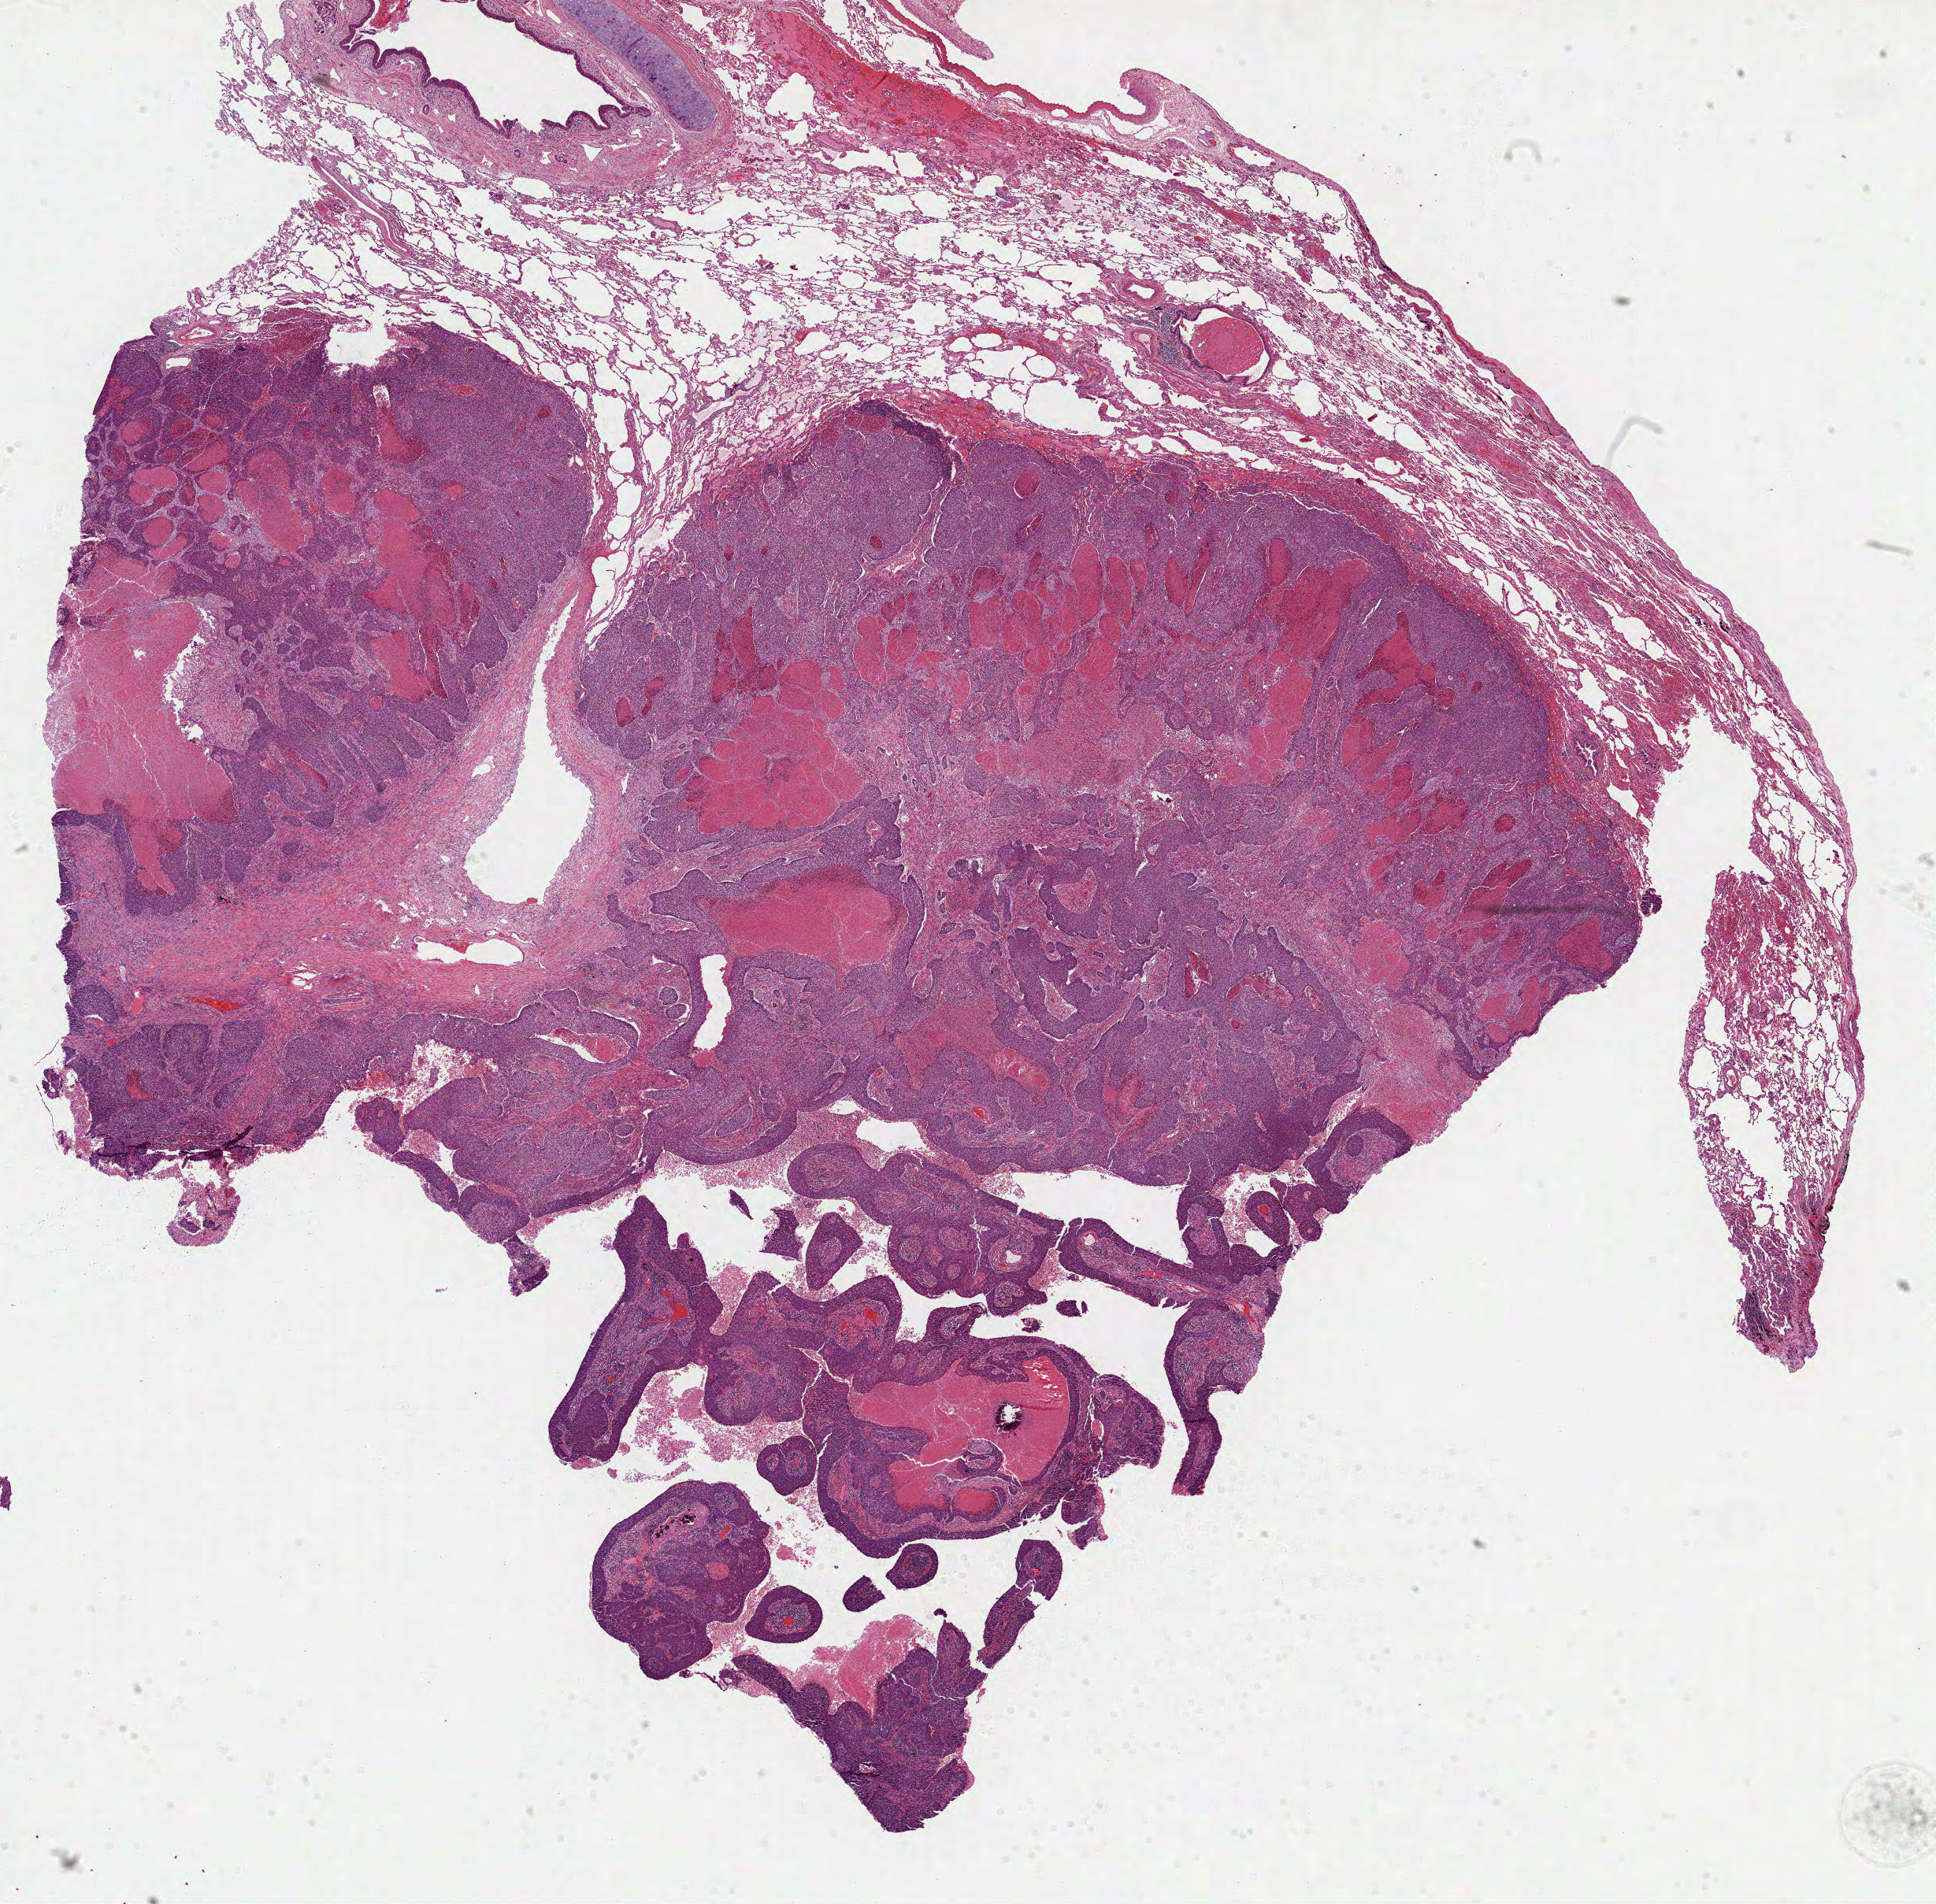
Whole-slide histology image, Hematoxylin and eosin (H&E) stained — a low-resolution overview of the entire scanned area, about 19.8 x 19.5 mm (acquisition: 40x scan), FFPE section, lung, primary tumour sample. Patient: female, age at initial diagnosis 78 years.
- AJCC pathologic stage: IB (7th edition)
- histologic diagnosis: Squamous cell carcinoma, NOS (upper lobe, lung)